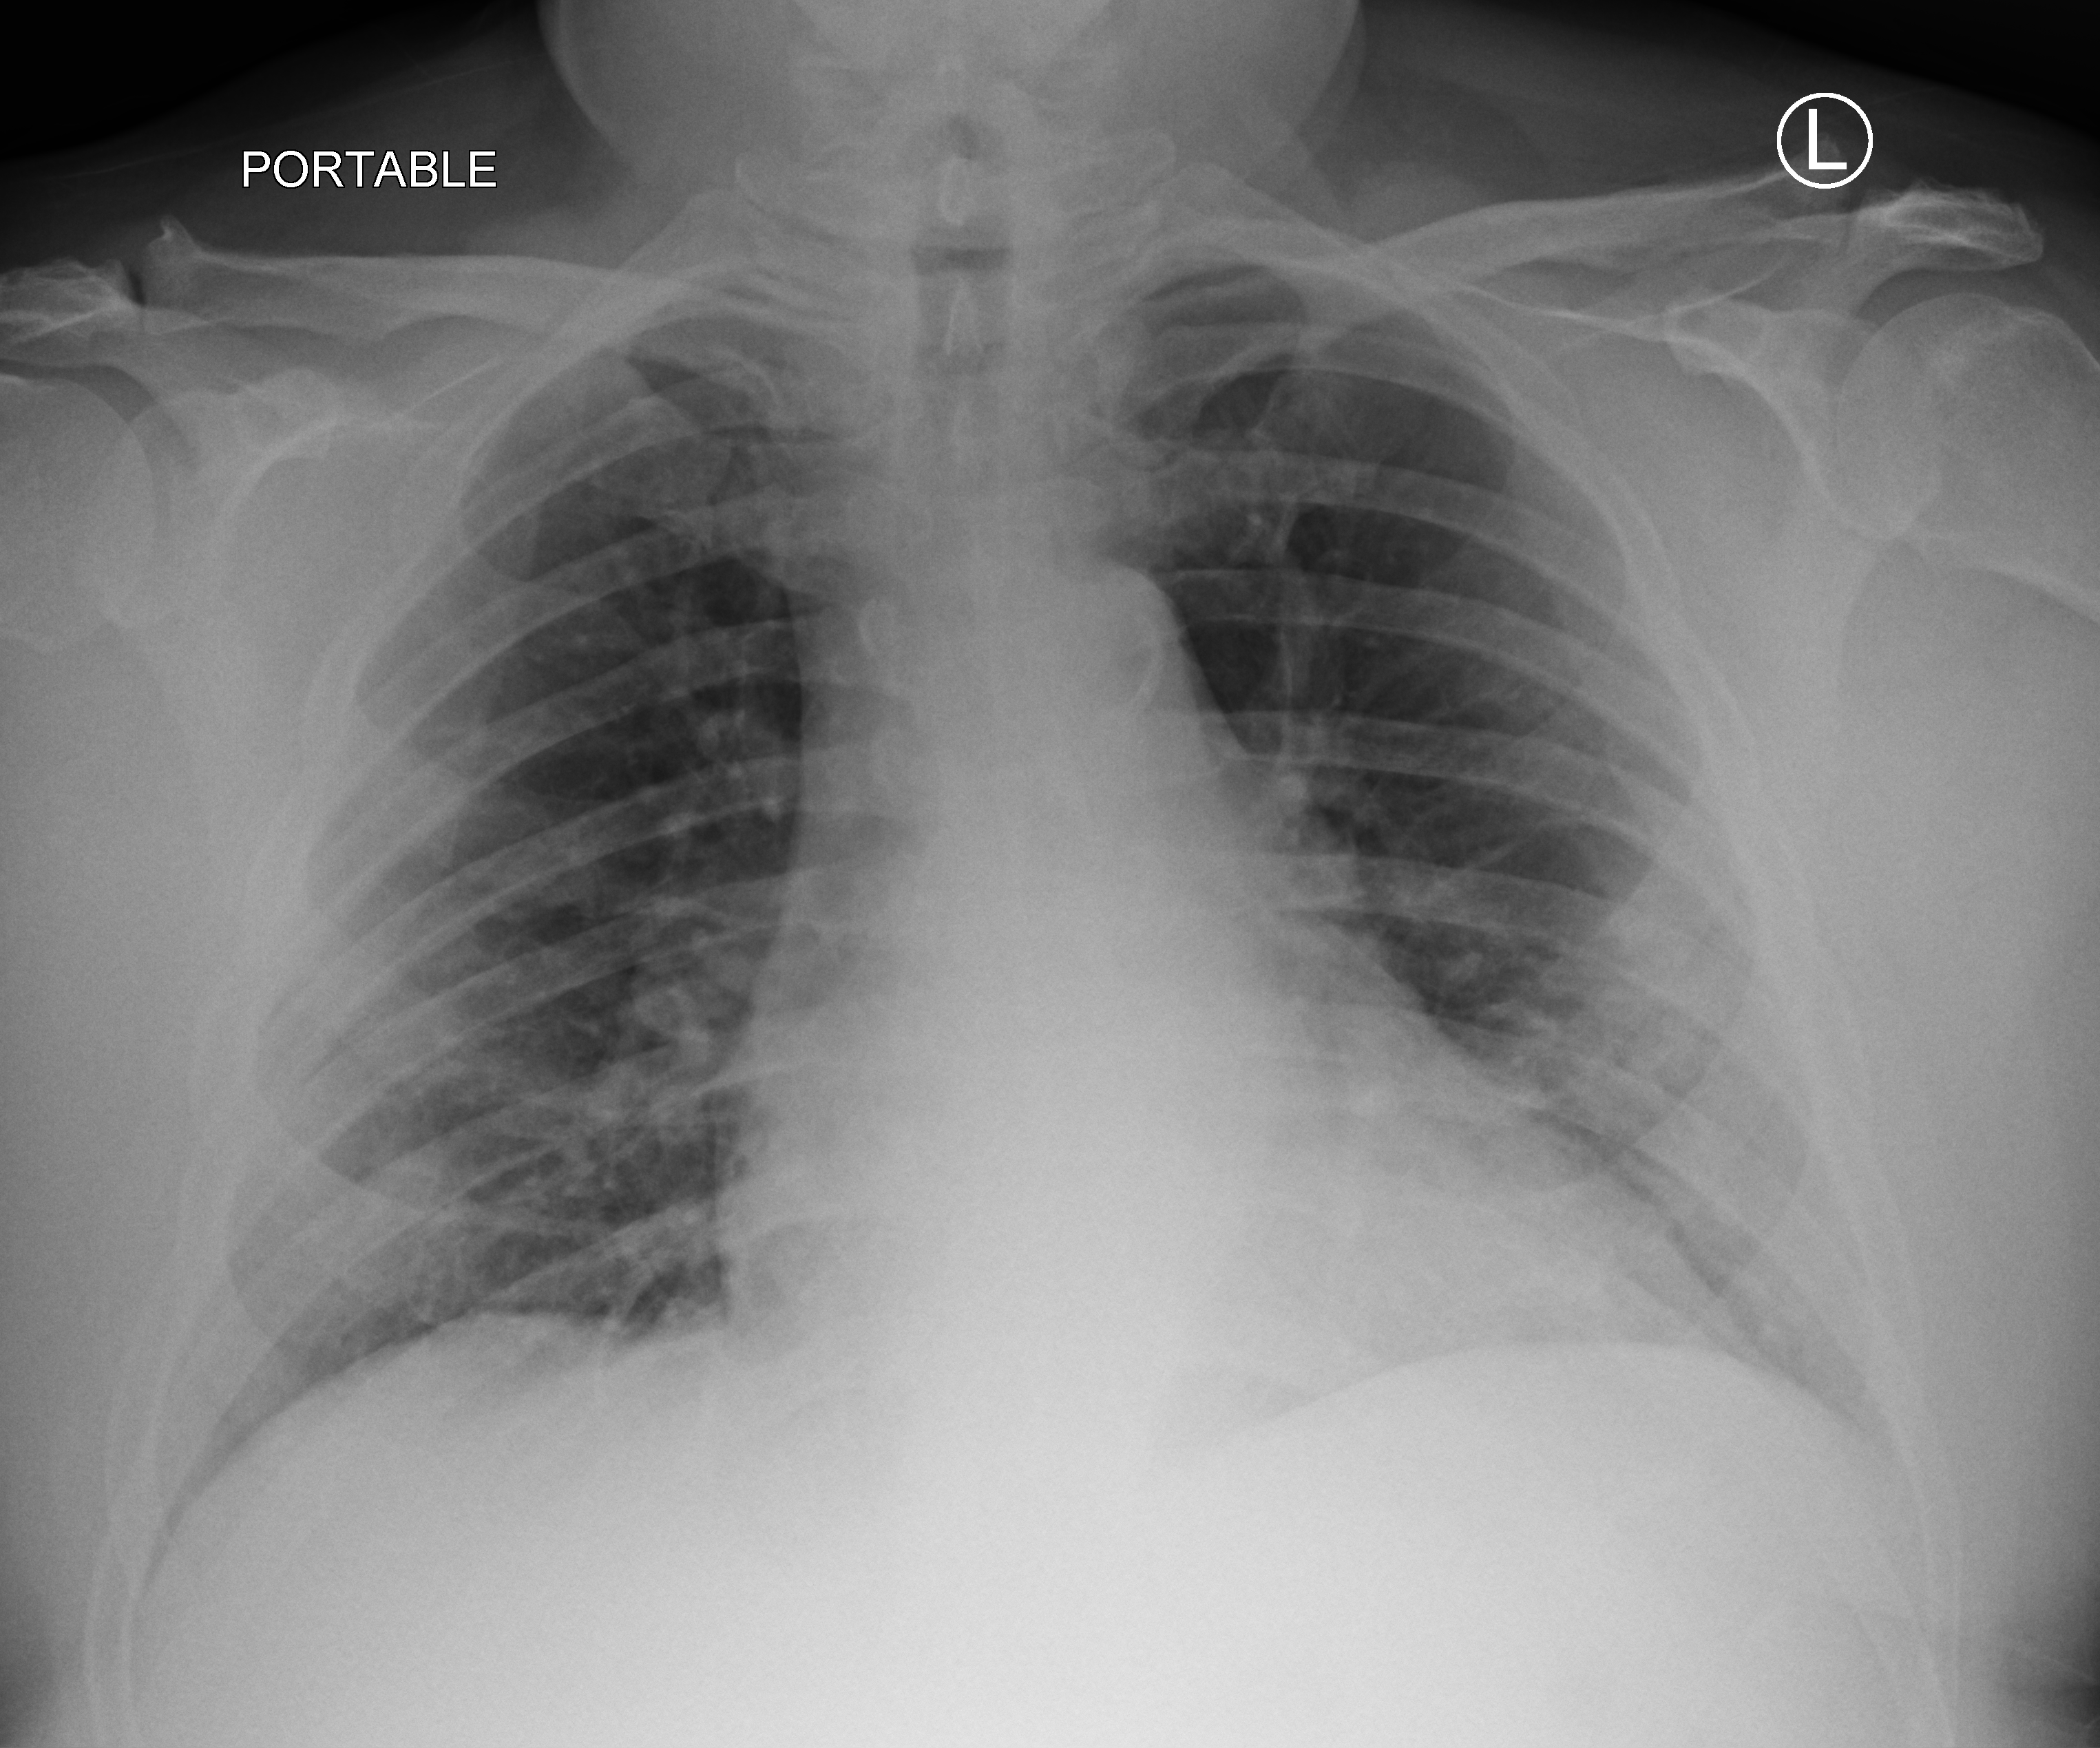
Bedside chest radiograph (computed radiography), anteroposterior (AP) projection. Patient hospitalised with COVID-19; male, aged 18–59 years.
Hospital-stay facts (about this admission, not read from this image; timing relative to this image not recorded):
- smoking status (admission record): former
- length of hospital stay: 3 days
- COPD (admission record): no